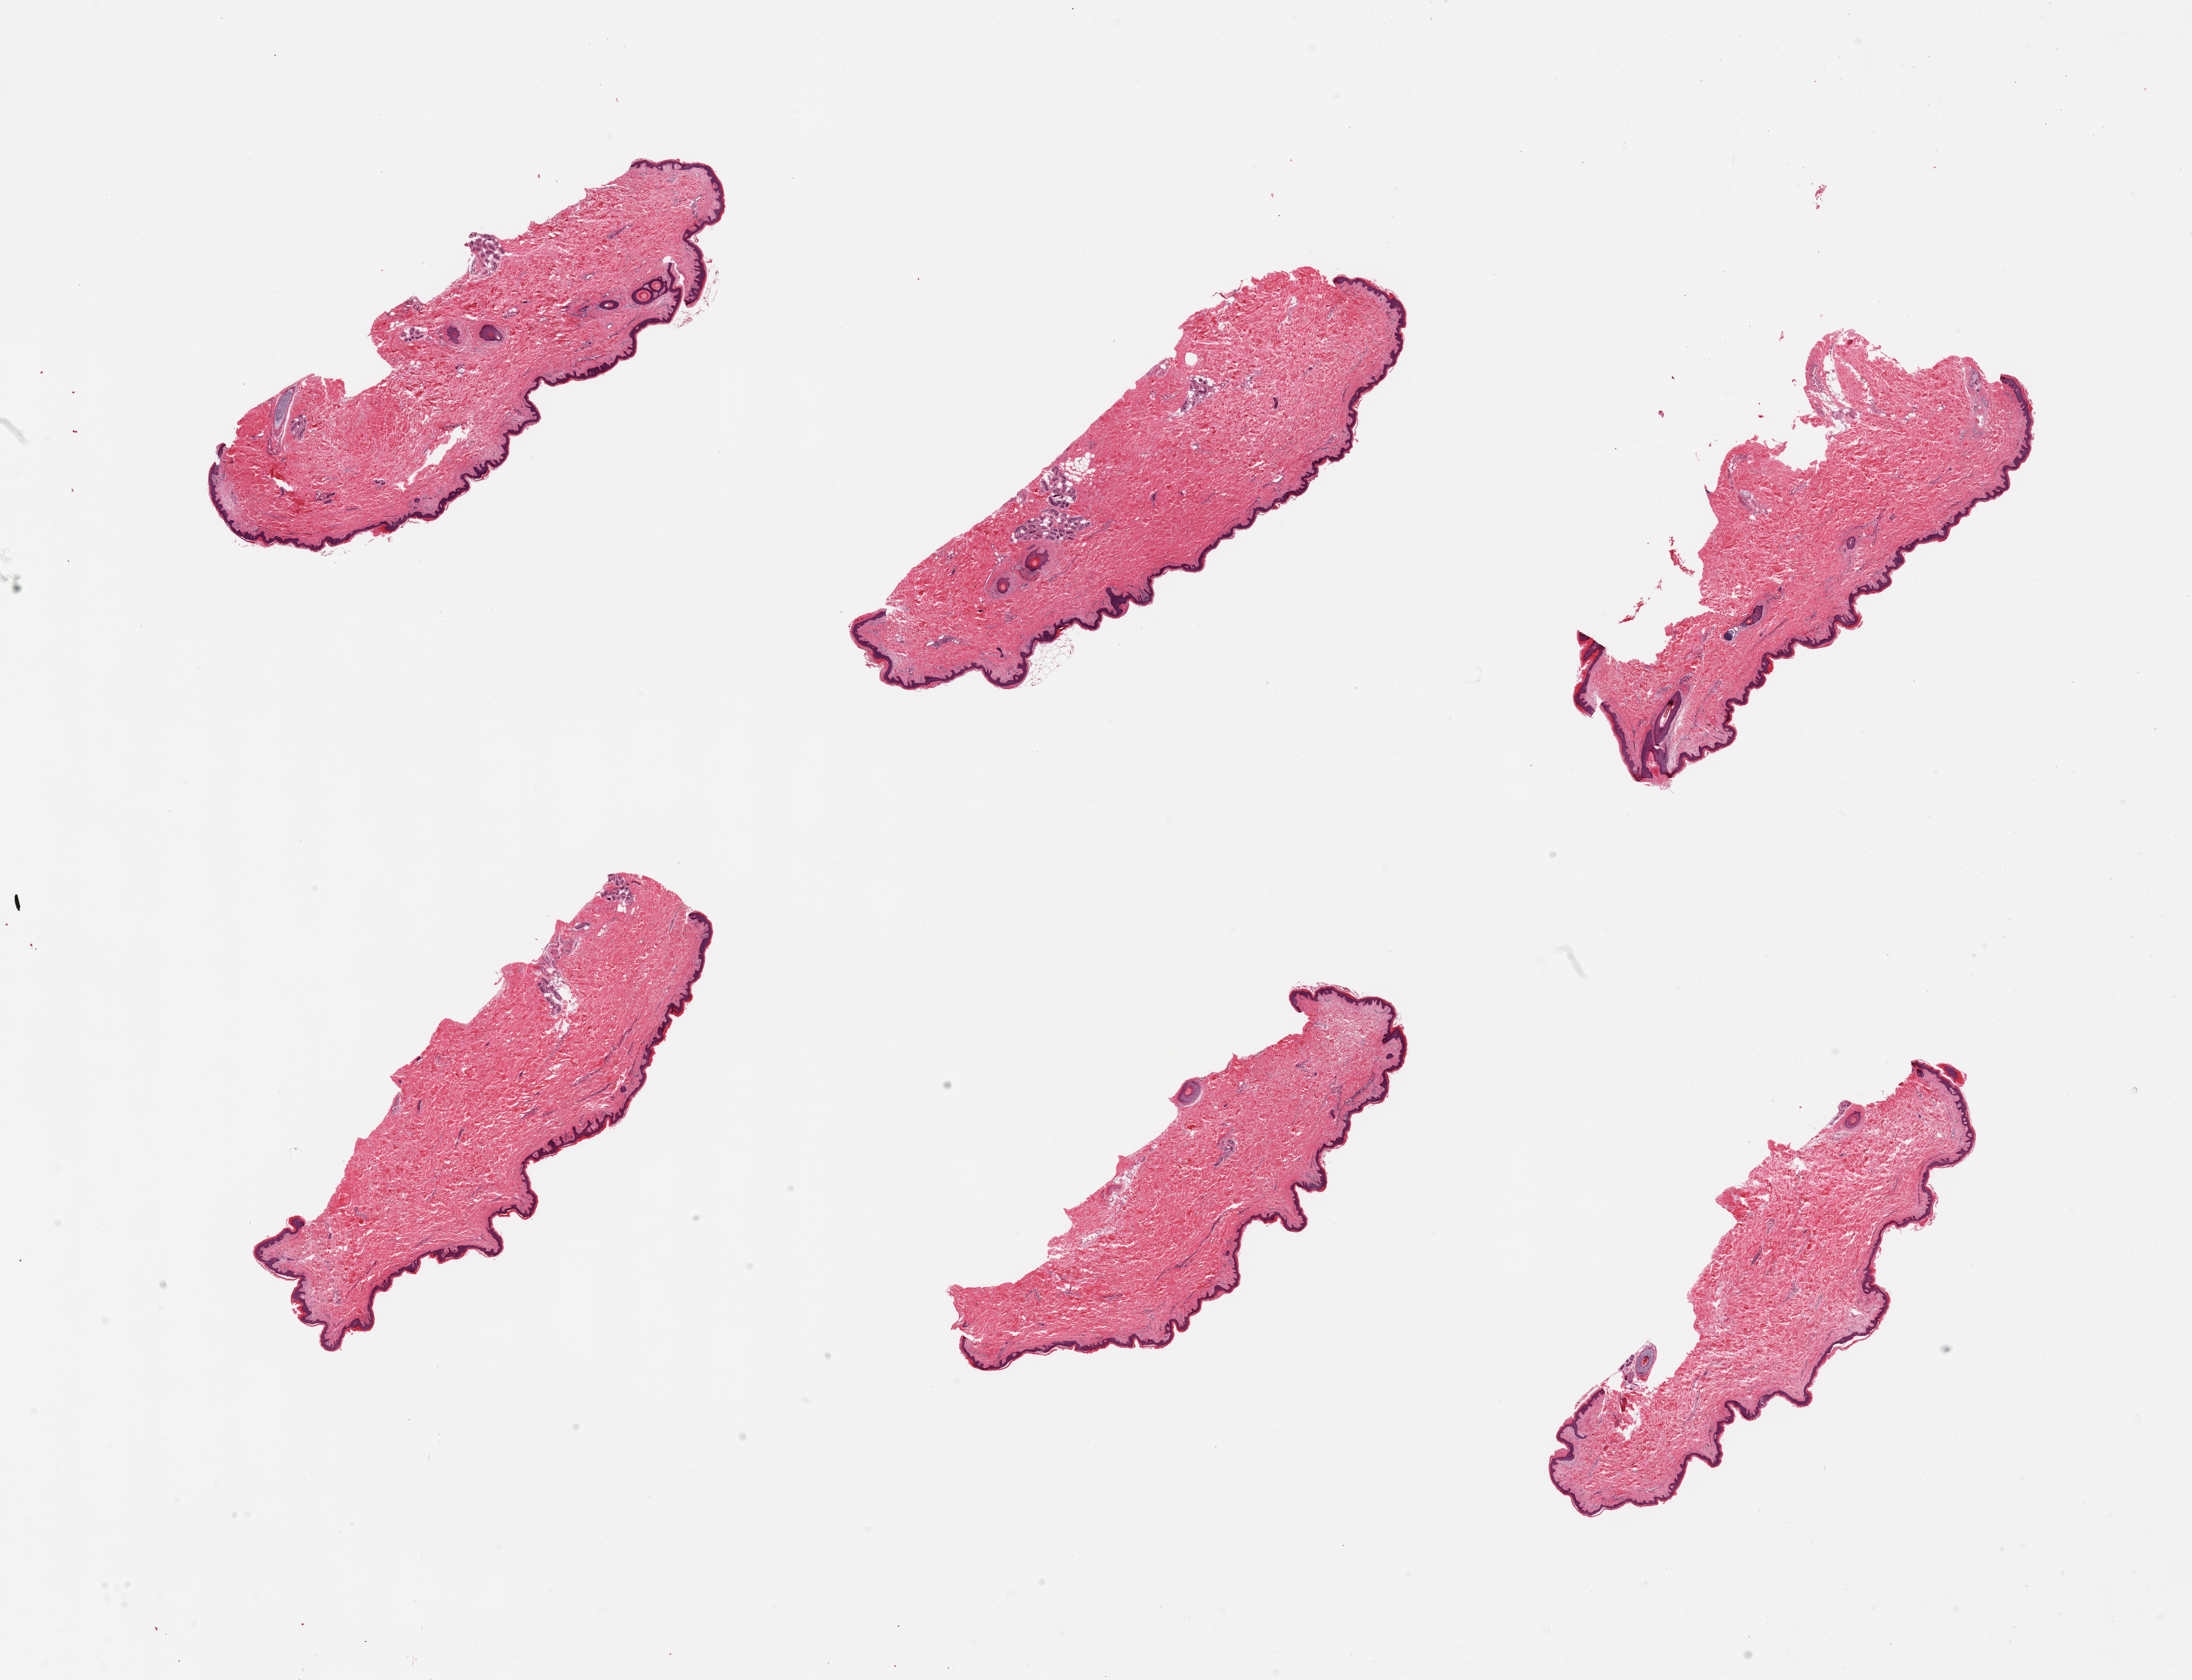
Digitized H&E-stained section, low-resolution overview of the scanned area, about 27.6 x 21.1 mm. PAXgene-fixed, paraffin-embedded tissue. Section of skin of suprapubic region (target tissue). Donor tissue sample.
Review note (as recorded): 6 pieces; hair bearing skin well trimmed.